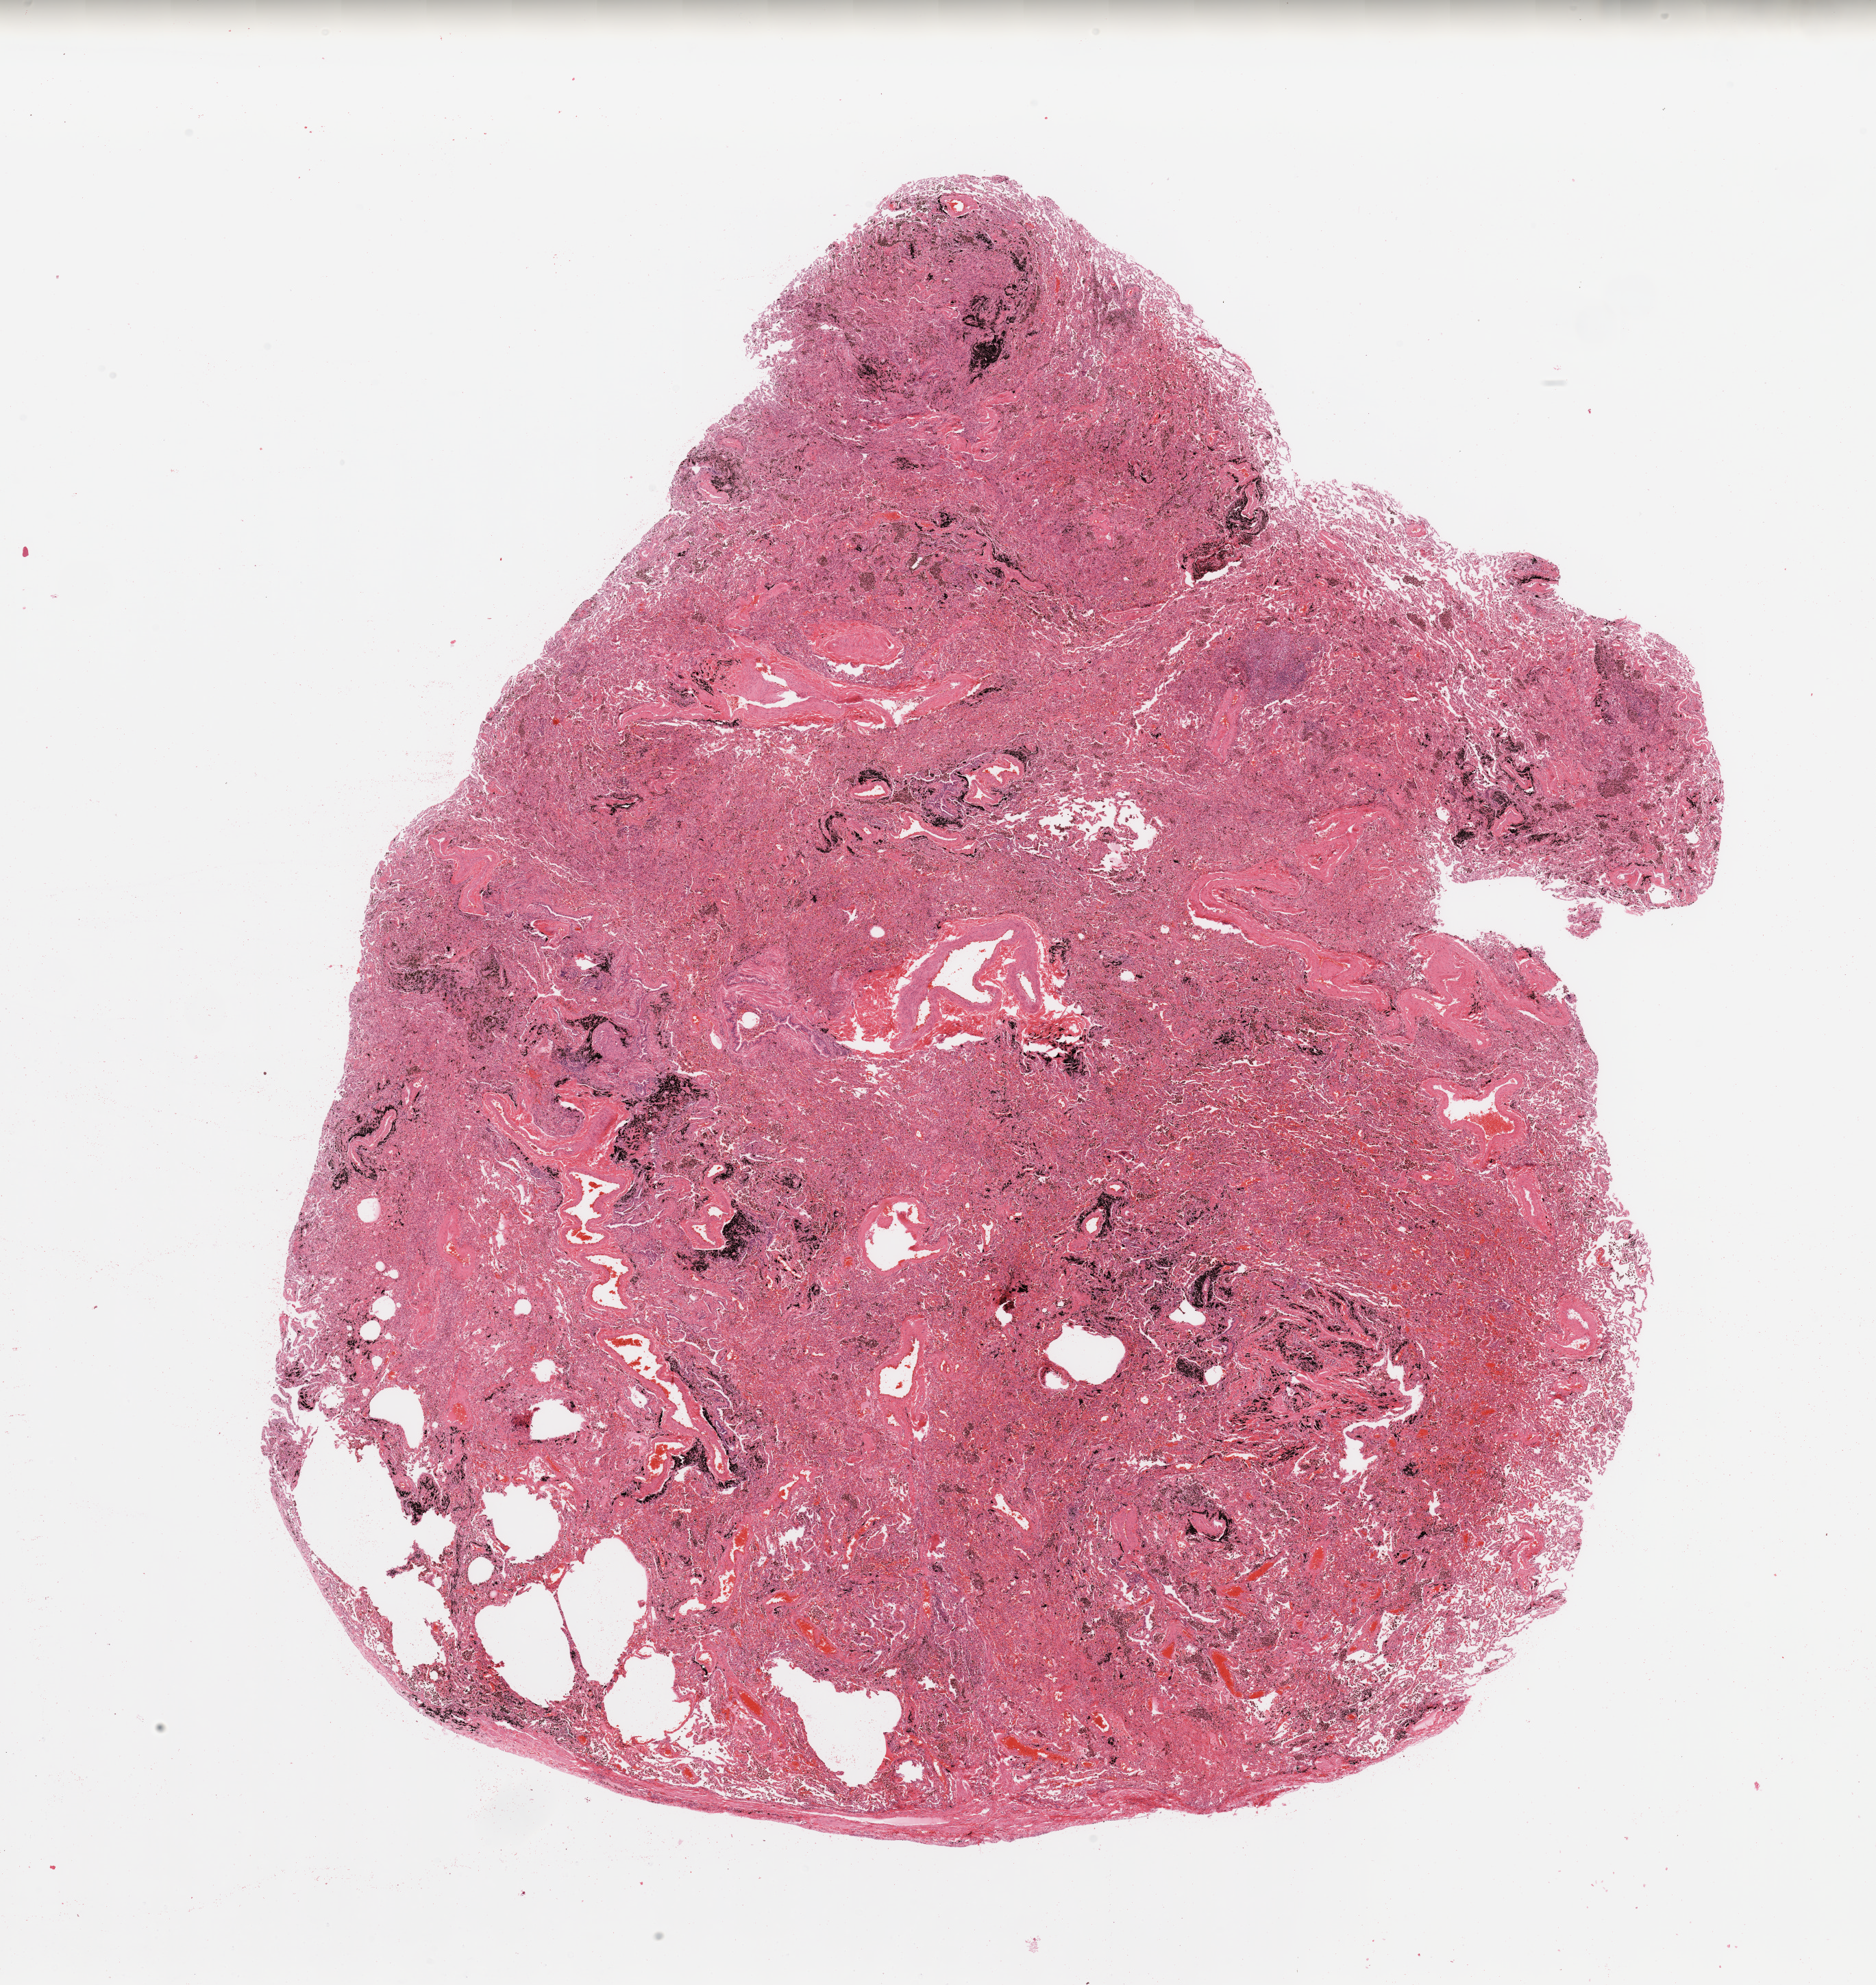
Hematoxylin and eosin (H&E) stained whole-slide image — a low-resolution overview of the entire scanned area, about 21.7 x 22.9 mm; normal (non-tumour) tissue sample, sampled site: lung. Male, 60 y/o.
This section: normal (non-tumour) tissue from the same patient. Patient diagnosis: Adenocarcinoma, NOS.